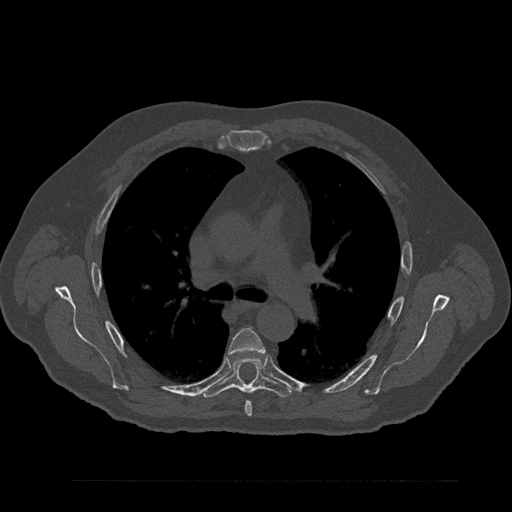
CT including the spine, one axial slice; position 574 of 797 along the scan axis; reconstruction kernel Br40s/3; 120 kVp; bone window (W 1800 / L 400 HU); 0.5 mm slice thickness; 512 × 512 image matrix, field of view 430 × 430 mm. Male patient, age 61 years. From the clinical record (not read from this slice): primary cancer: prostate.
Structures marked on this image (semi-automatically segmented with operator editing):
- T5 vertebra: bounding box <229,328,266,416> (left, top, right, bottom; pixels)
- T6 vertebra: <201,356,293,398>